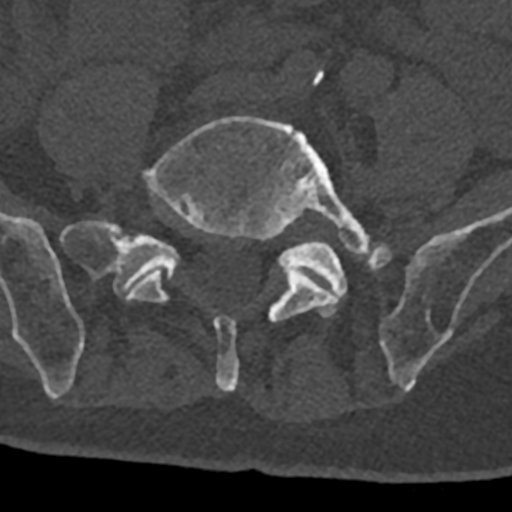
CT including the spine, one axial slice; slice 184 of 797 in the series (ordered by position); bone window (W 1800 / L 400 HU); 0.5 mm slice thickness; 512 × 512 image matrix, field of view 160 × 160 mm. Male patient, age 74 years. Case-level facts recorded for this patient, not image findings: primary cancer: renal; vertebrae with lytic lesions (as recorded): T10, L1, L2, L3, L4, L5.
Structures marked on this image (semi-automatic segmentation, software-assisted and operator-edited):
- L4 vertebra: bounding box <313,70,324,86> (left, top, right, bottom; pixels)
- L5 vertebra: <127,116,371,392>